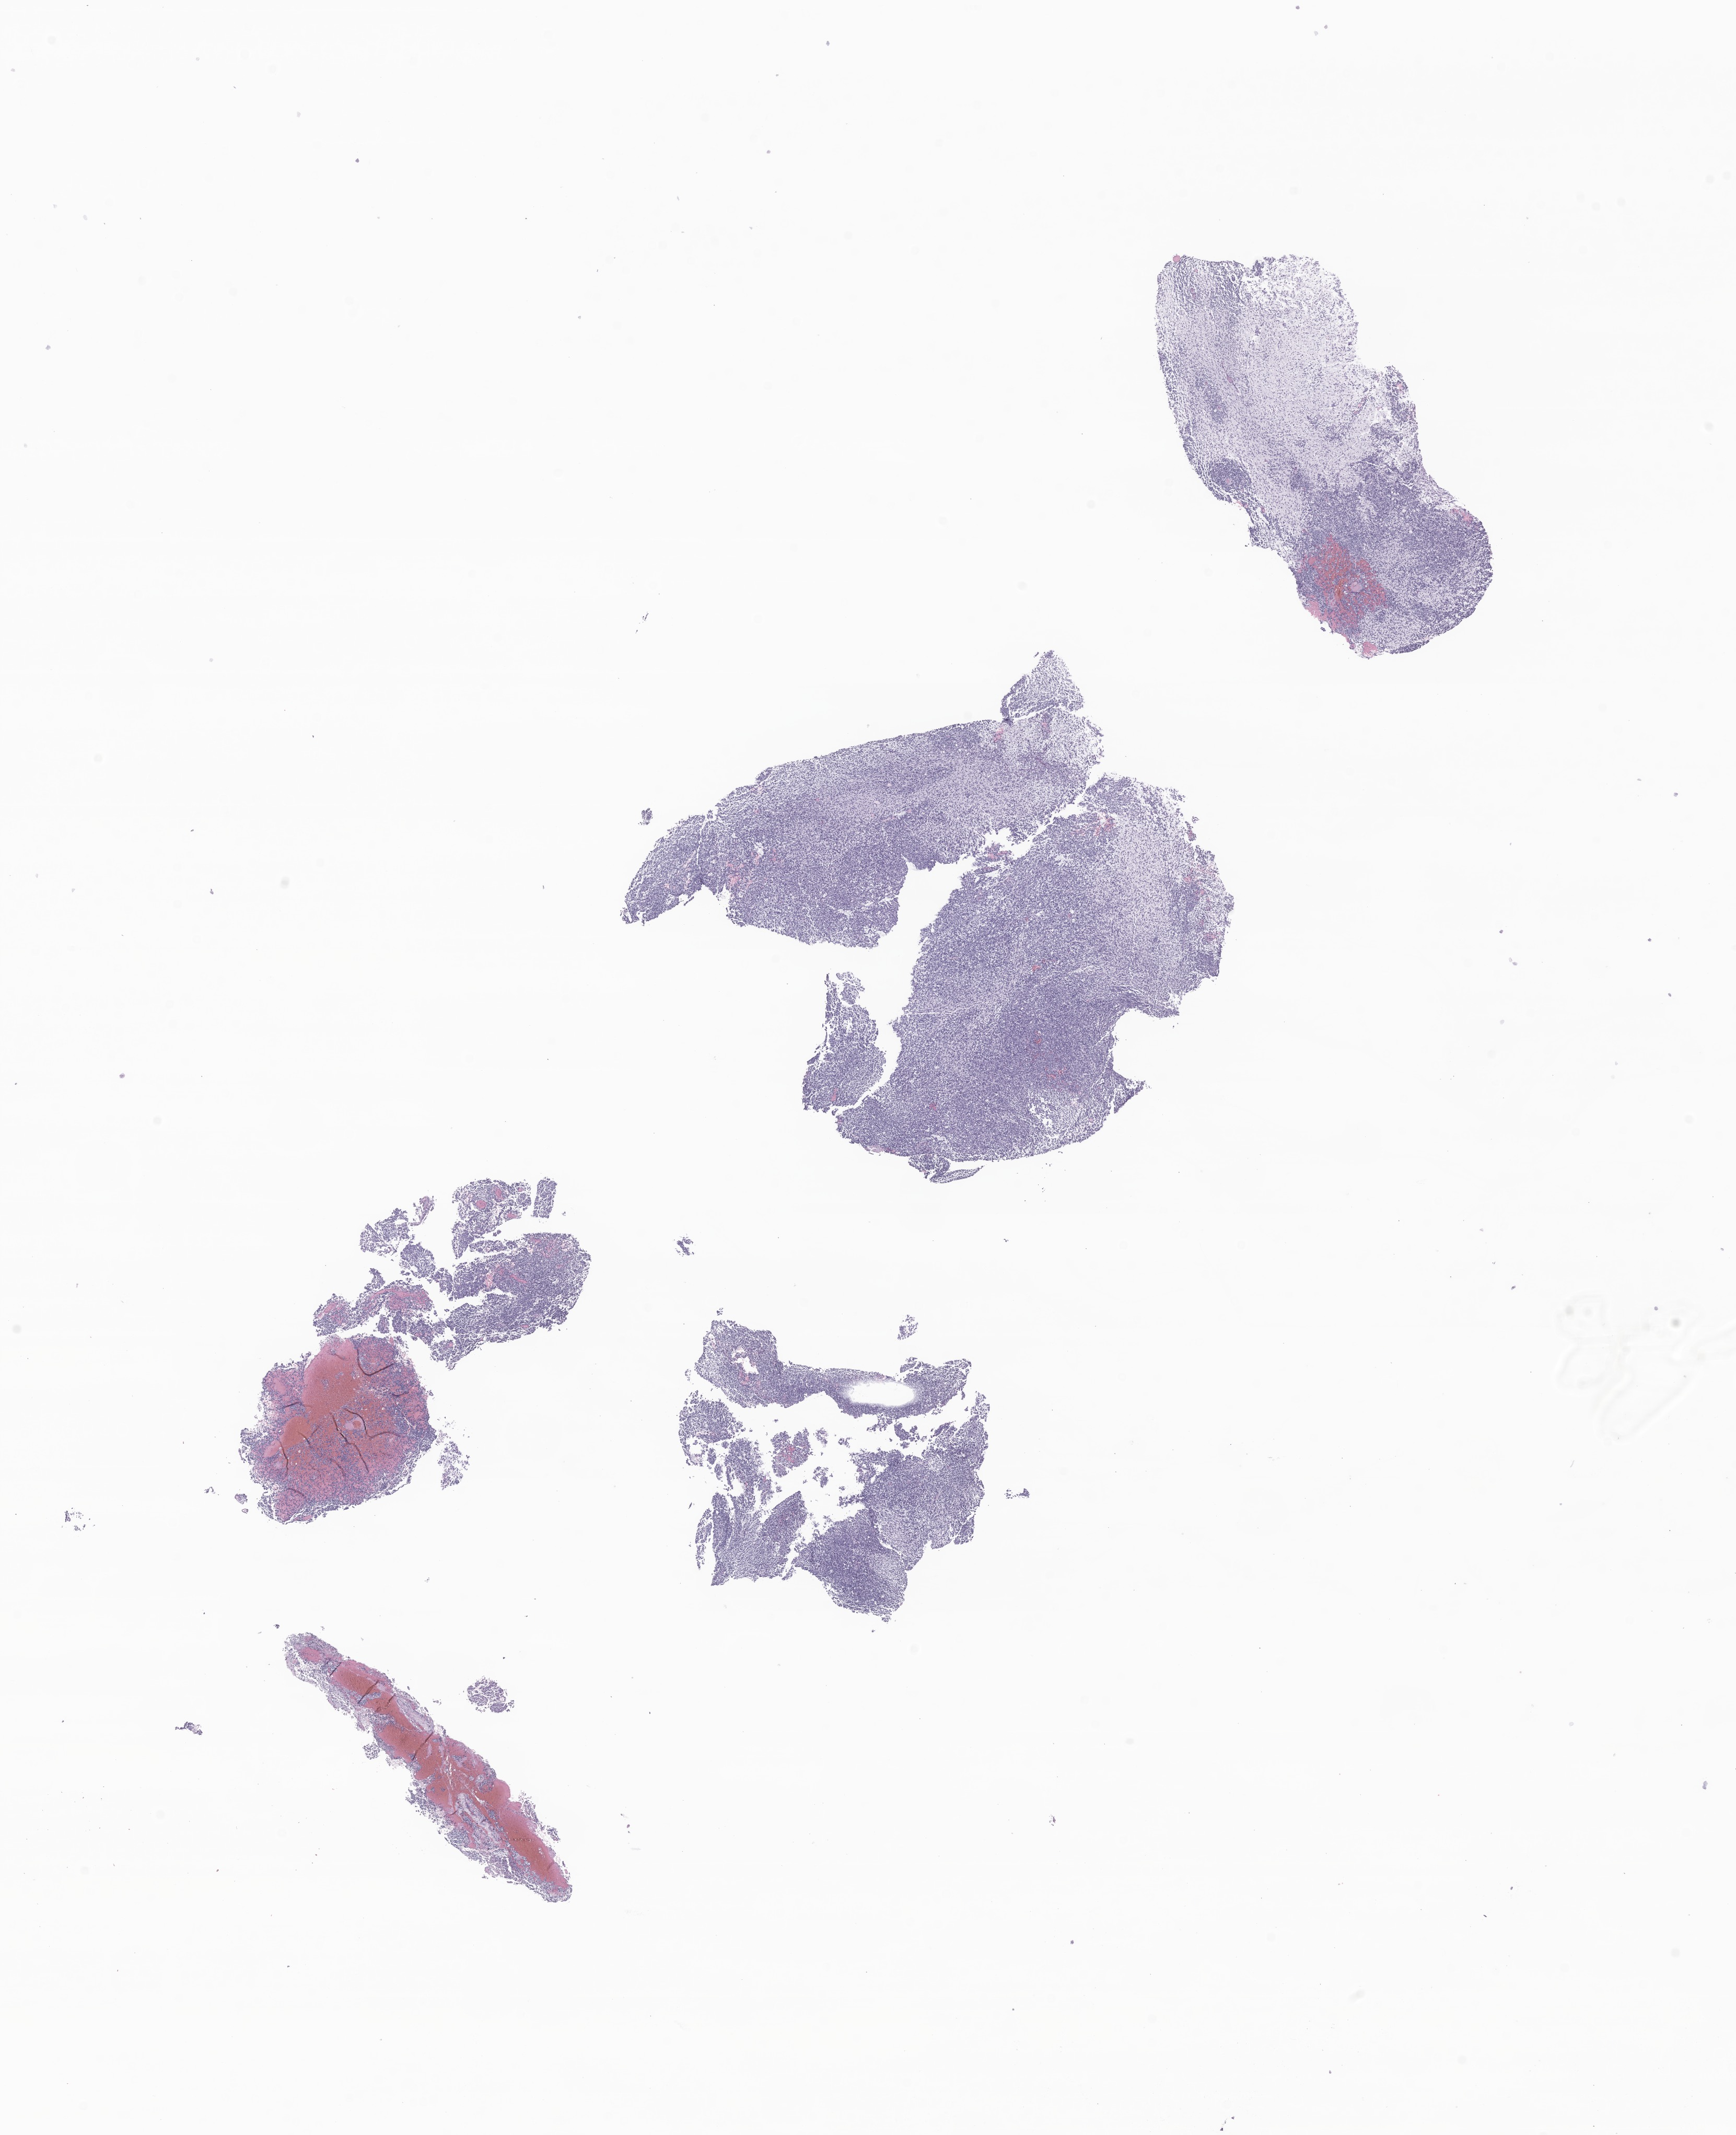
Digitized H&E-stained section of tumor tissue from the cerebellum, whole scanned area (about 14.0 x 17.2 mm) shown as a low-resolution overview, formalin-fixed, paraffin-embedded (FFPE) tissue. Patient male; age 893 days (about 2.4 years).
* recorded diagnosis: Atypical teratoid/rhabdoid tumor